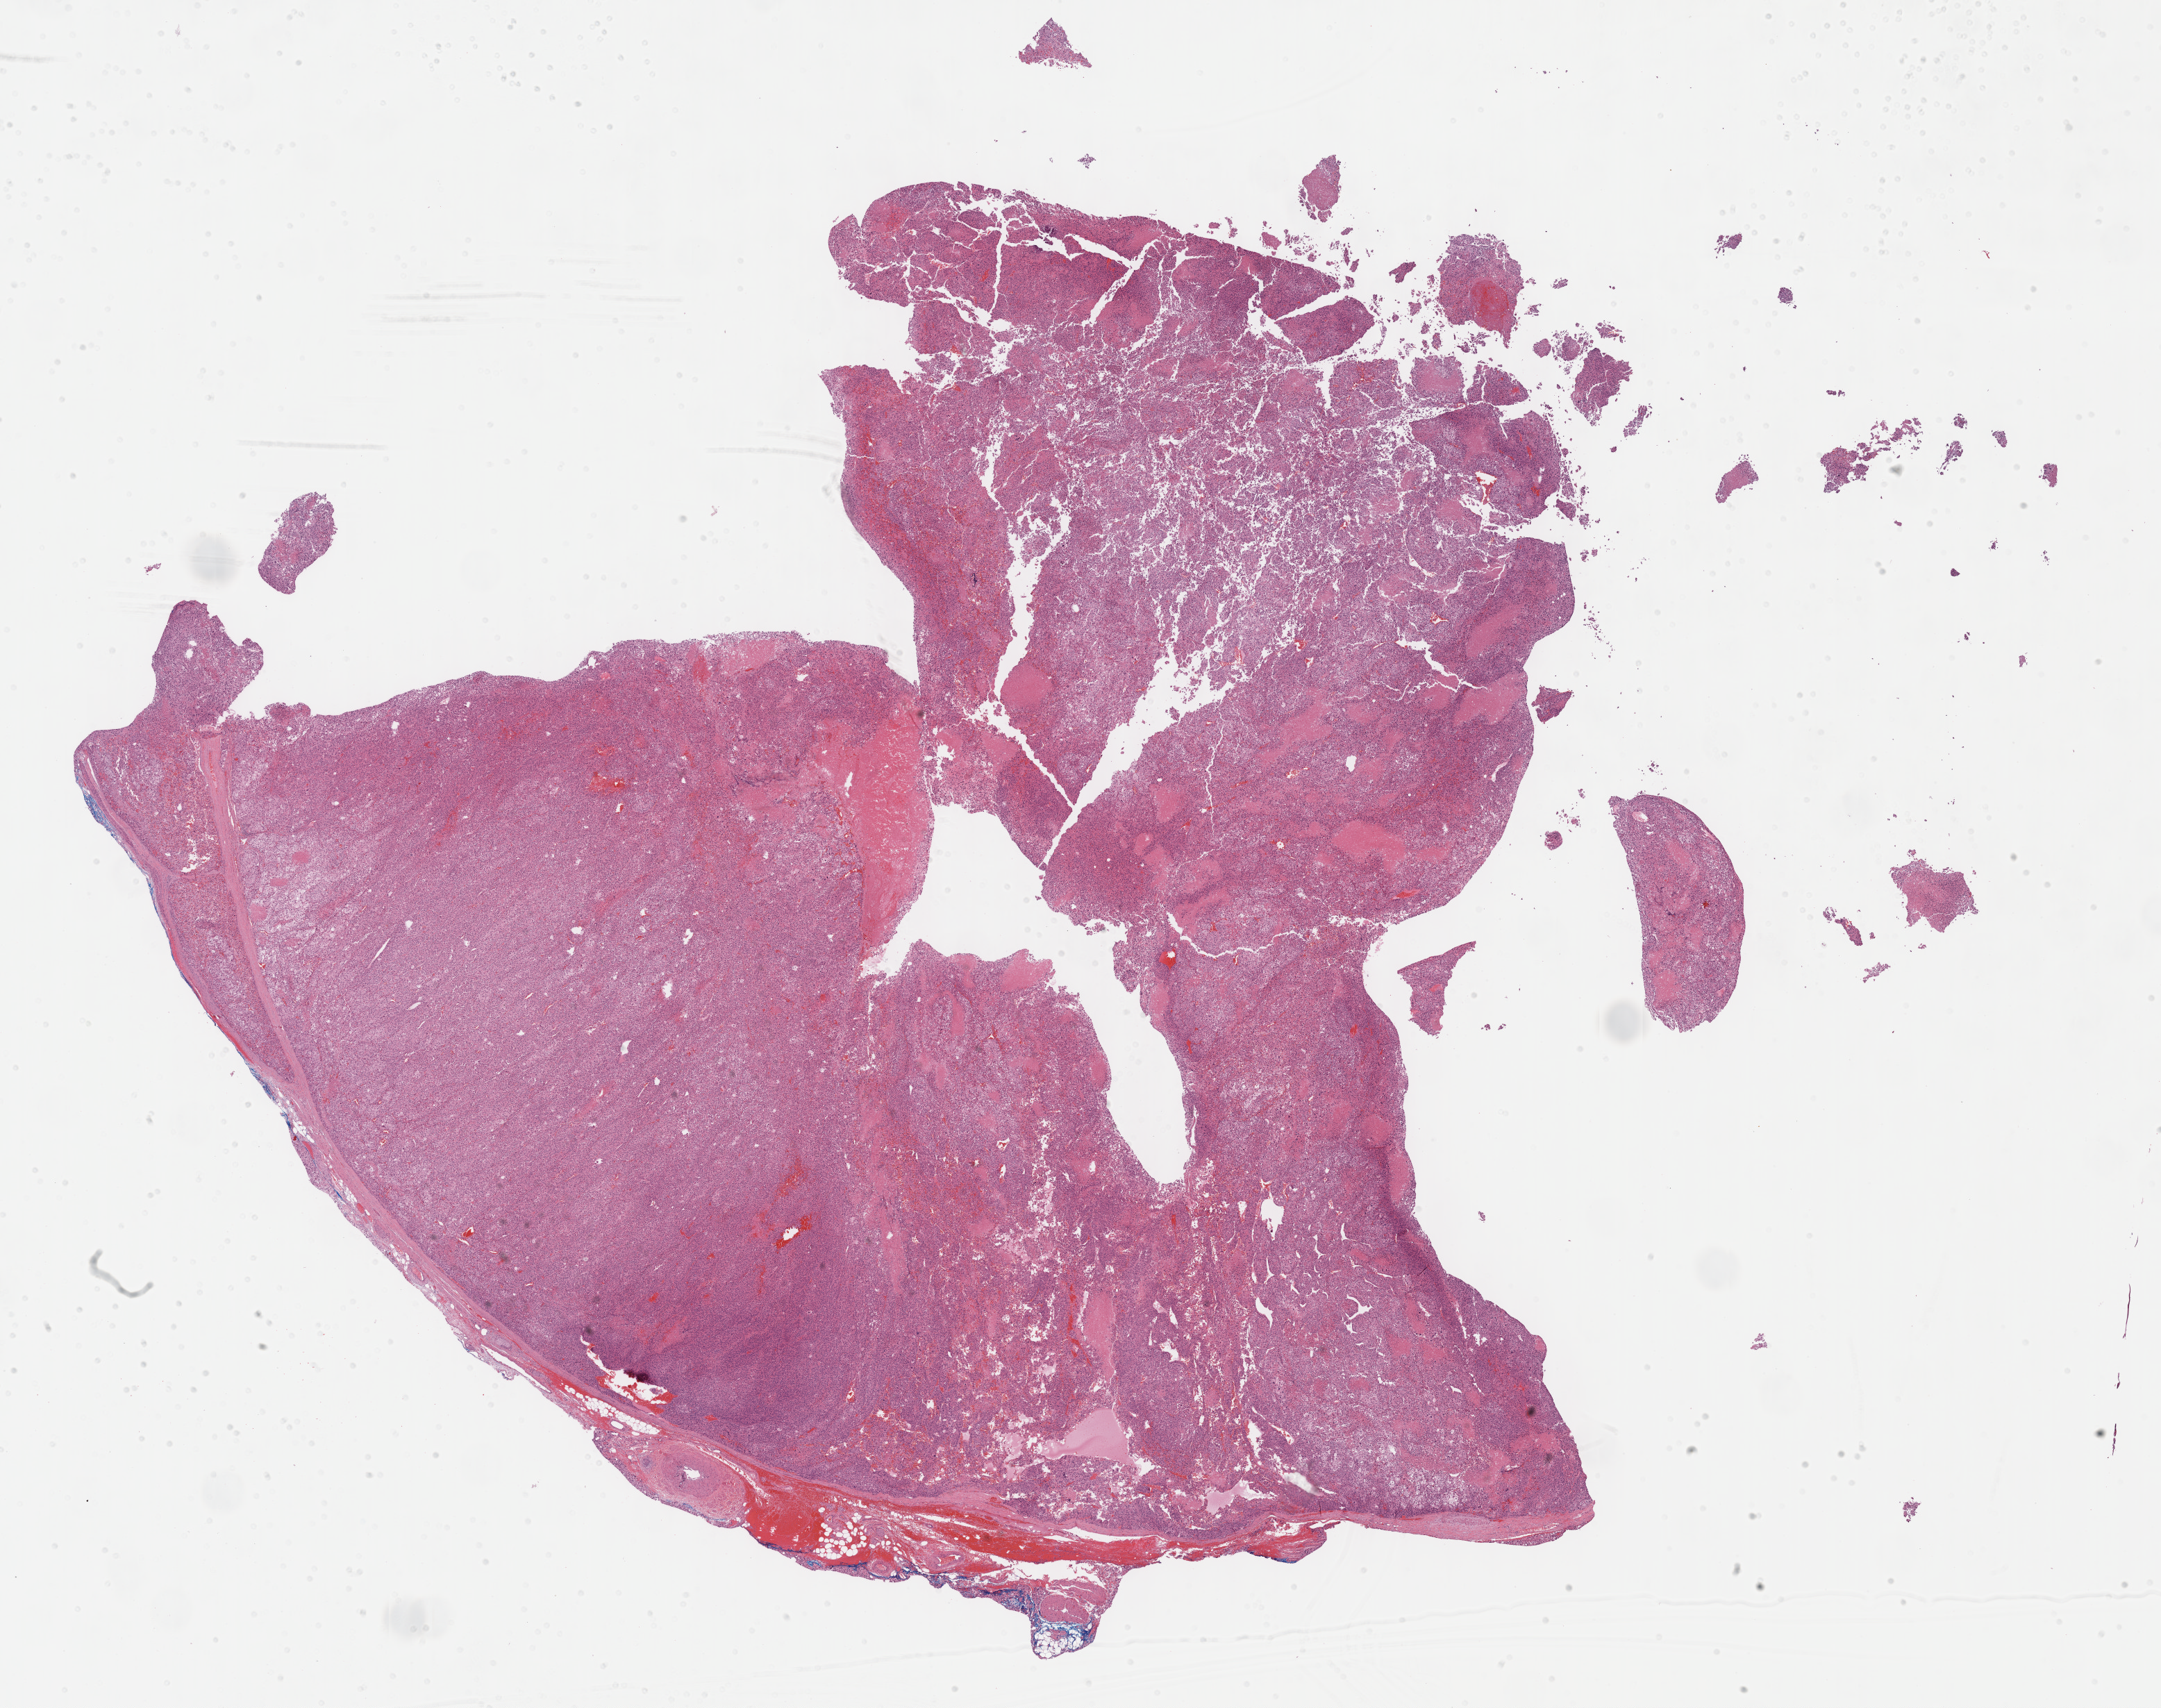
Hematoxylin and eosin (H&E) stained whole-slide image — a low-resolution overview of the entire scanned area, about 25.2 x 19.9 mm. FFPE section. Sample: primary tumour, adrenal cortex. Female patient; age at initial diagnosis 68 years.
Lymph nodes positive (case pathology): 1 of 2 examined. Pathologic diagnosis: Adrenal cortical carcinoma (cortex of adrenal gland).